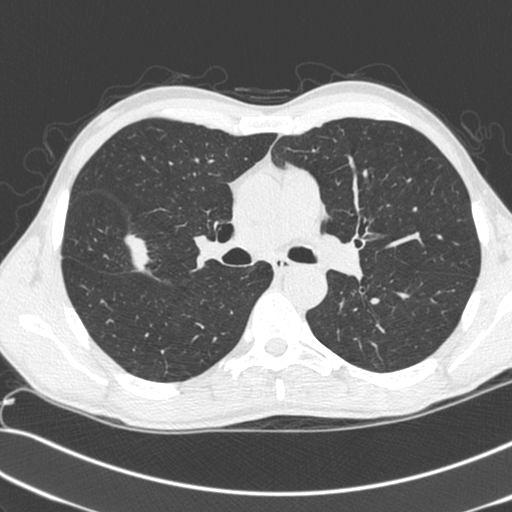
Chest CT (low-dose screening protocol), one axial image; baseline annual screen; lung window (W 1500 / L -600 HU); 1.3 mm slice thickness; slice 98 of 281 in the series; 512 × 512 image matrix. Male, age 55 years at enrolment.
• Expert-annotated lung lesion, box from (x=65, y=214) to (x=158, y=293) px.
• Reader record for this screening exam (exam-level; its link to the box is not recorded): non-calcified nodule or mass ≥4 mm, right upper lobe, 52 × 39 mm, spiculated (stellate) margins, soft tissue attenuation.
• Official screen result: positive, change unspecified: nodule(s) >= 4 mm or enlarging nodule(s), mass(es), or other non-specific abnormalities suspicious for lung cancer.